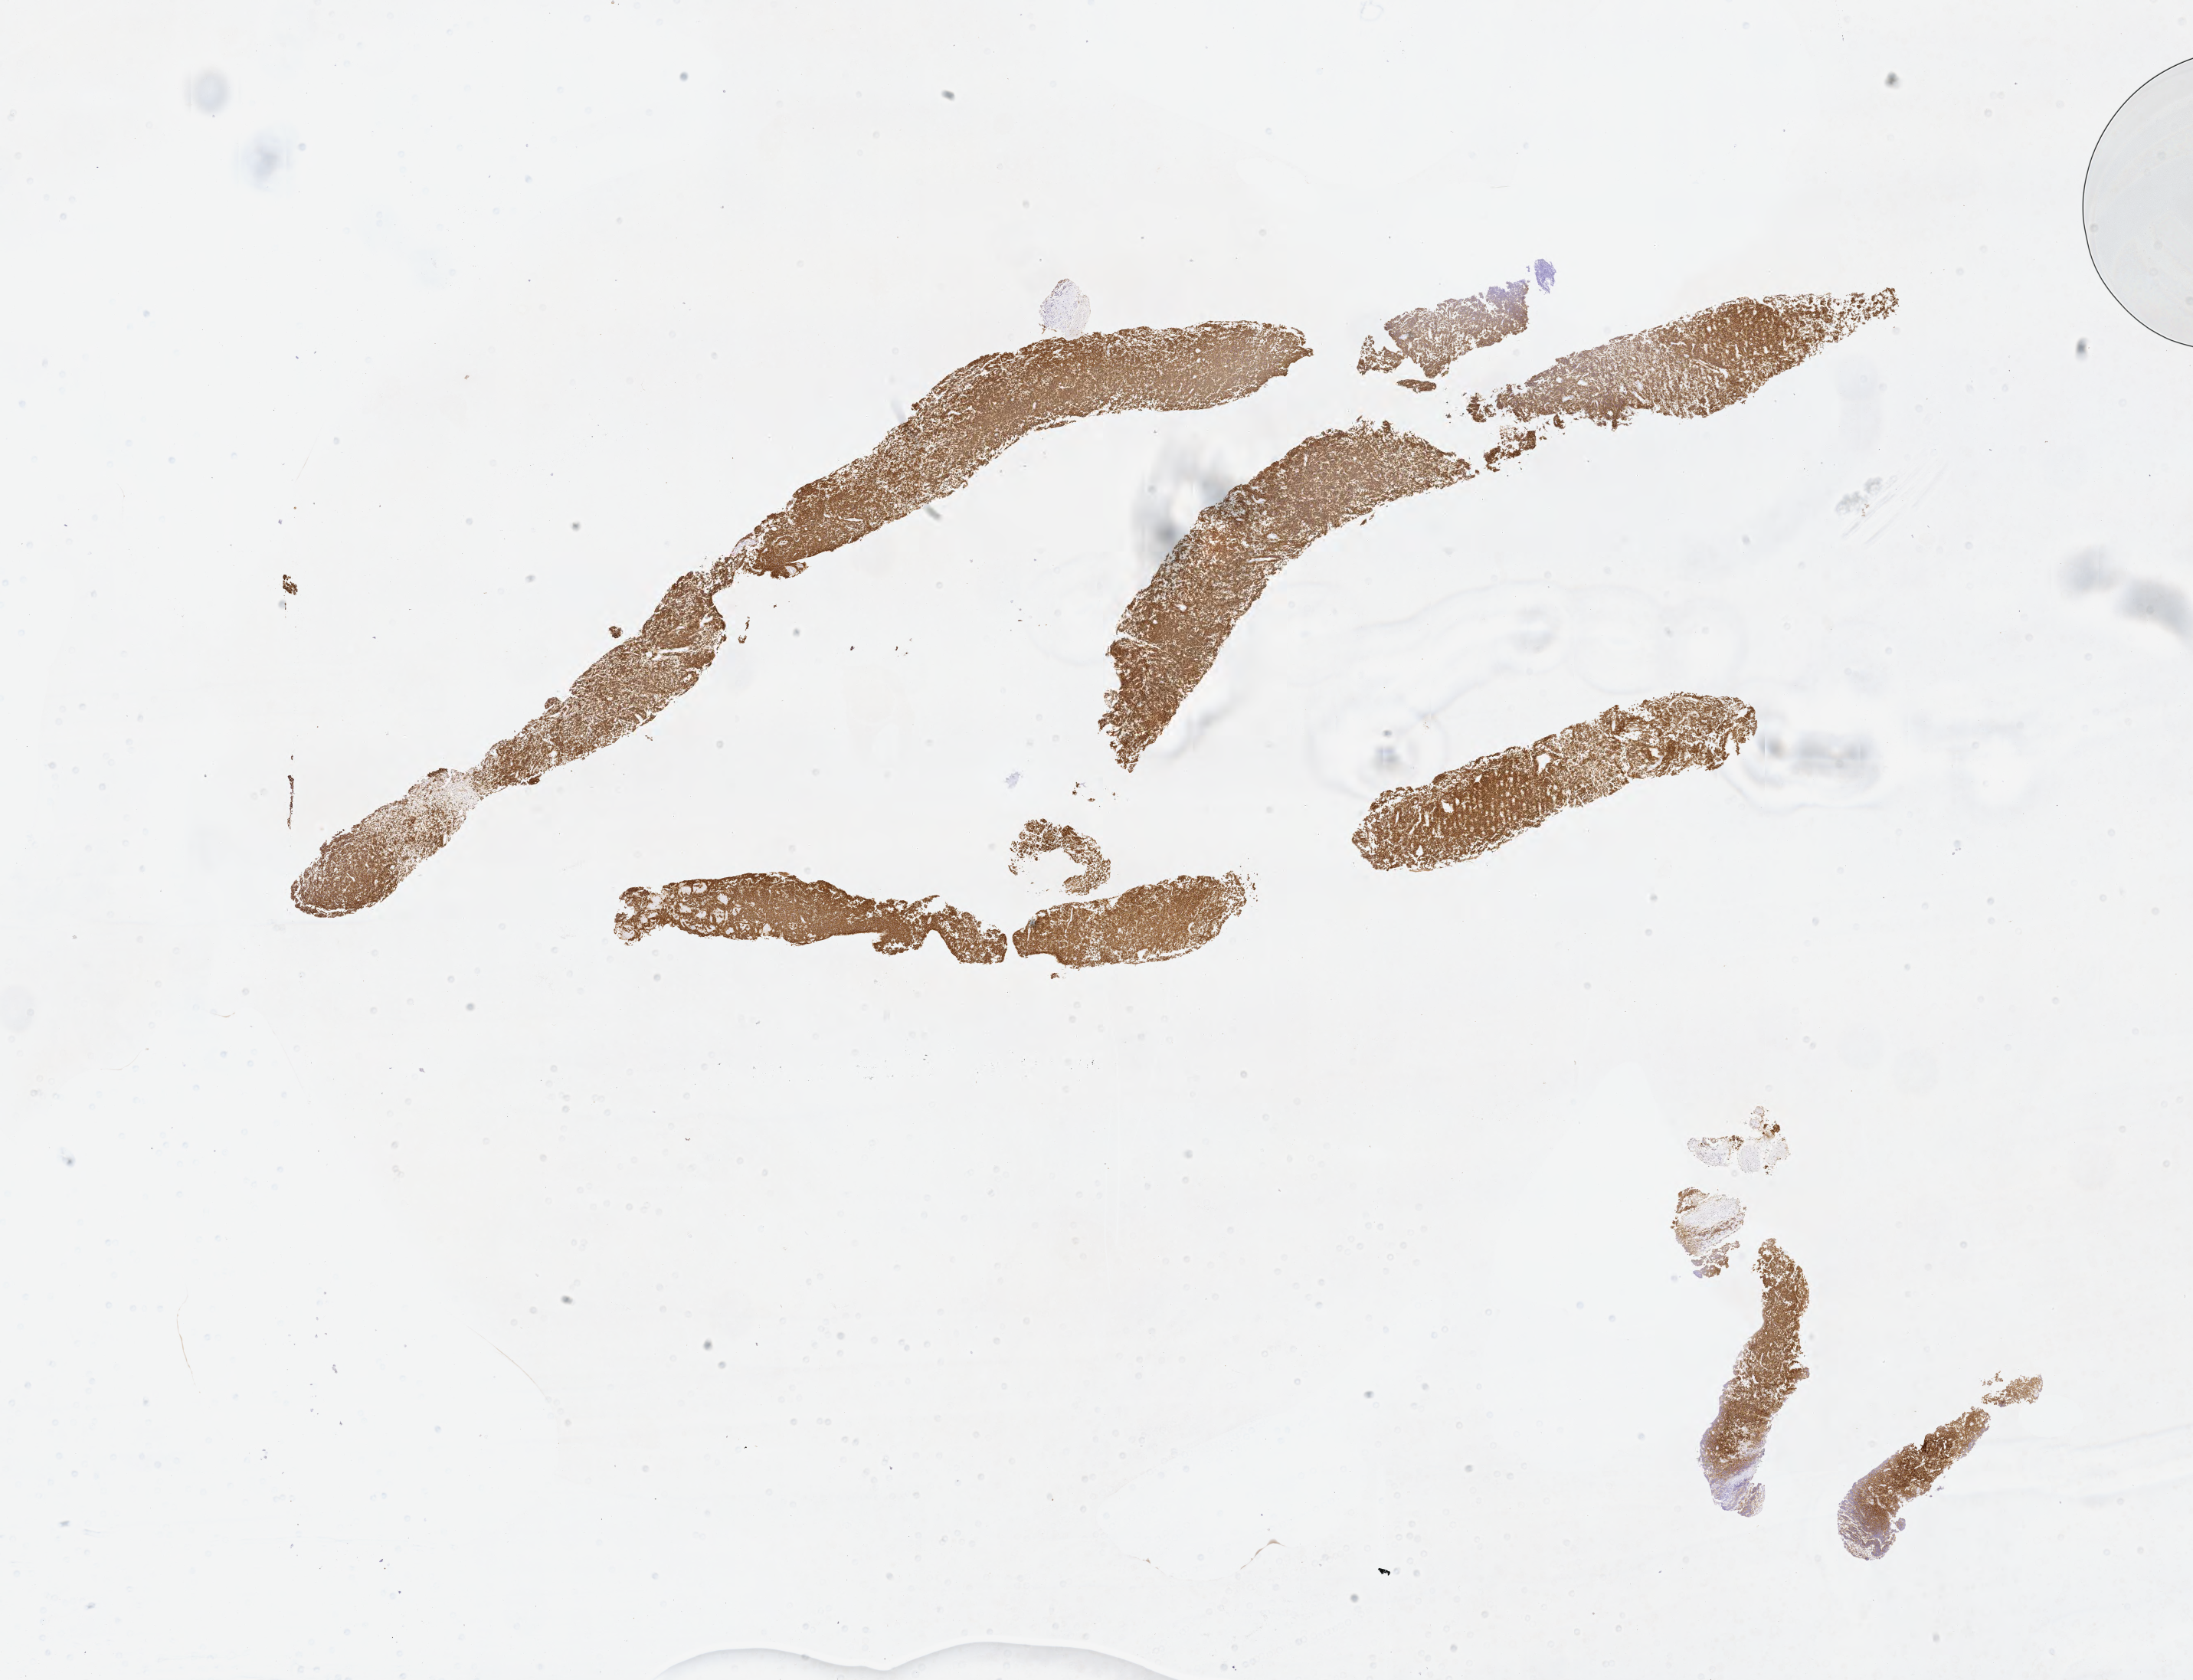
Immunohistochemistry (IHC) whole-slide image stained for CD20 — shown as a low-resolution overview of the whole scanned area (about 23.1 x 17.7 mm). Tumor tissue. Patient: male, age 66 years.
Diagnosis: Burkitt lymphoma, NOS.